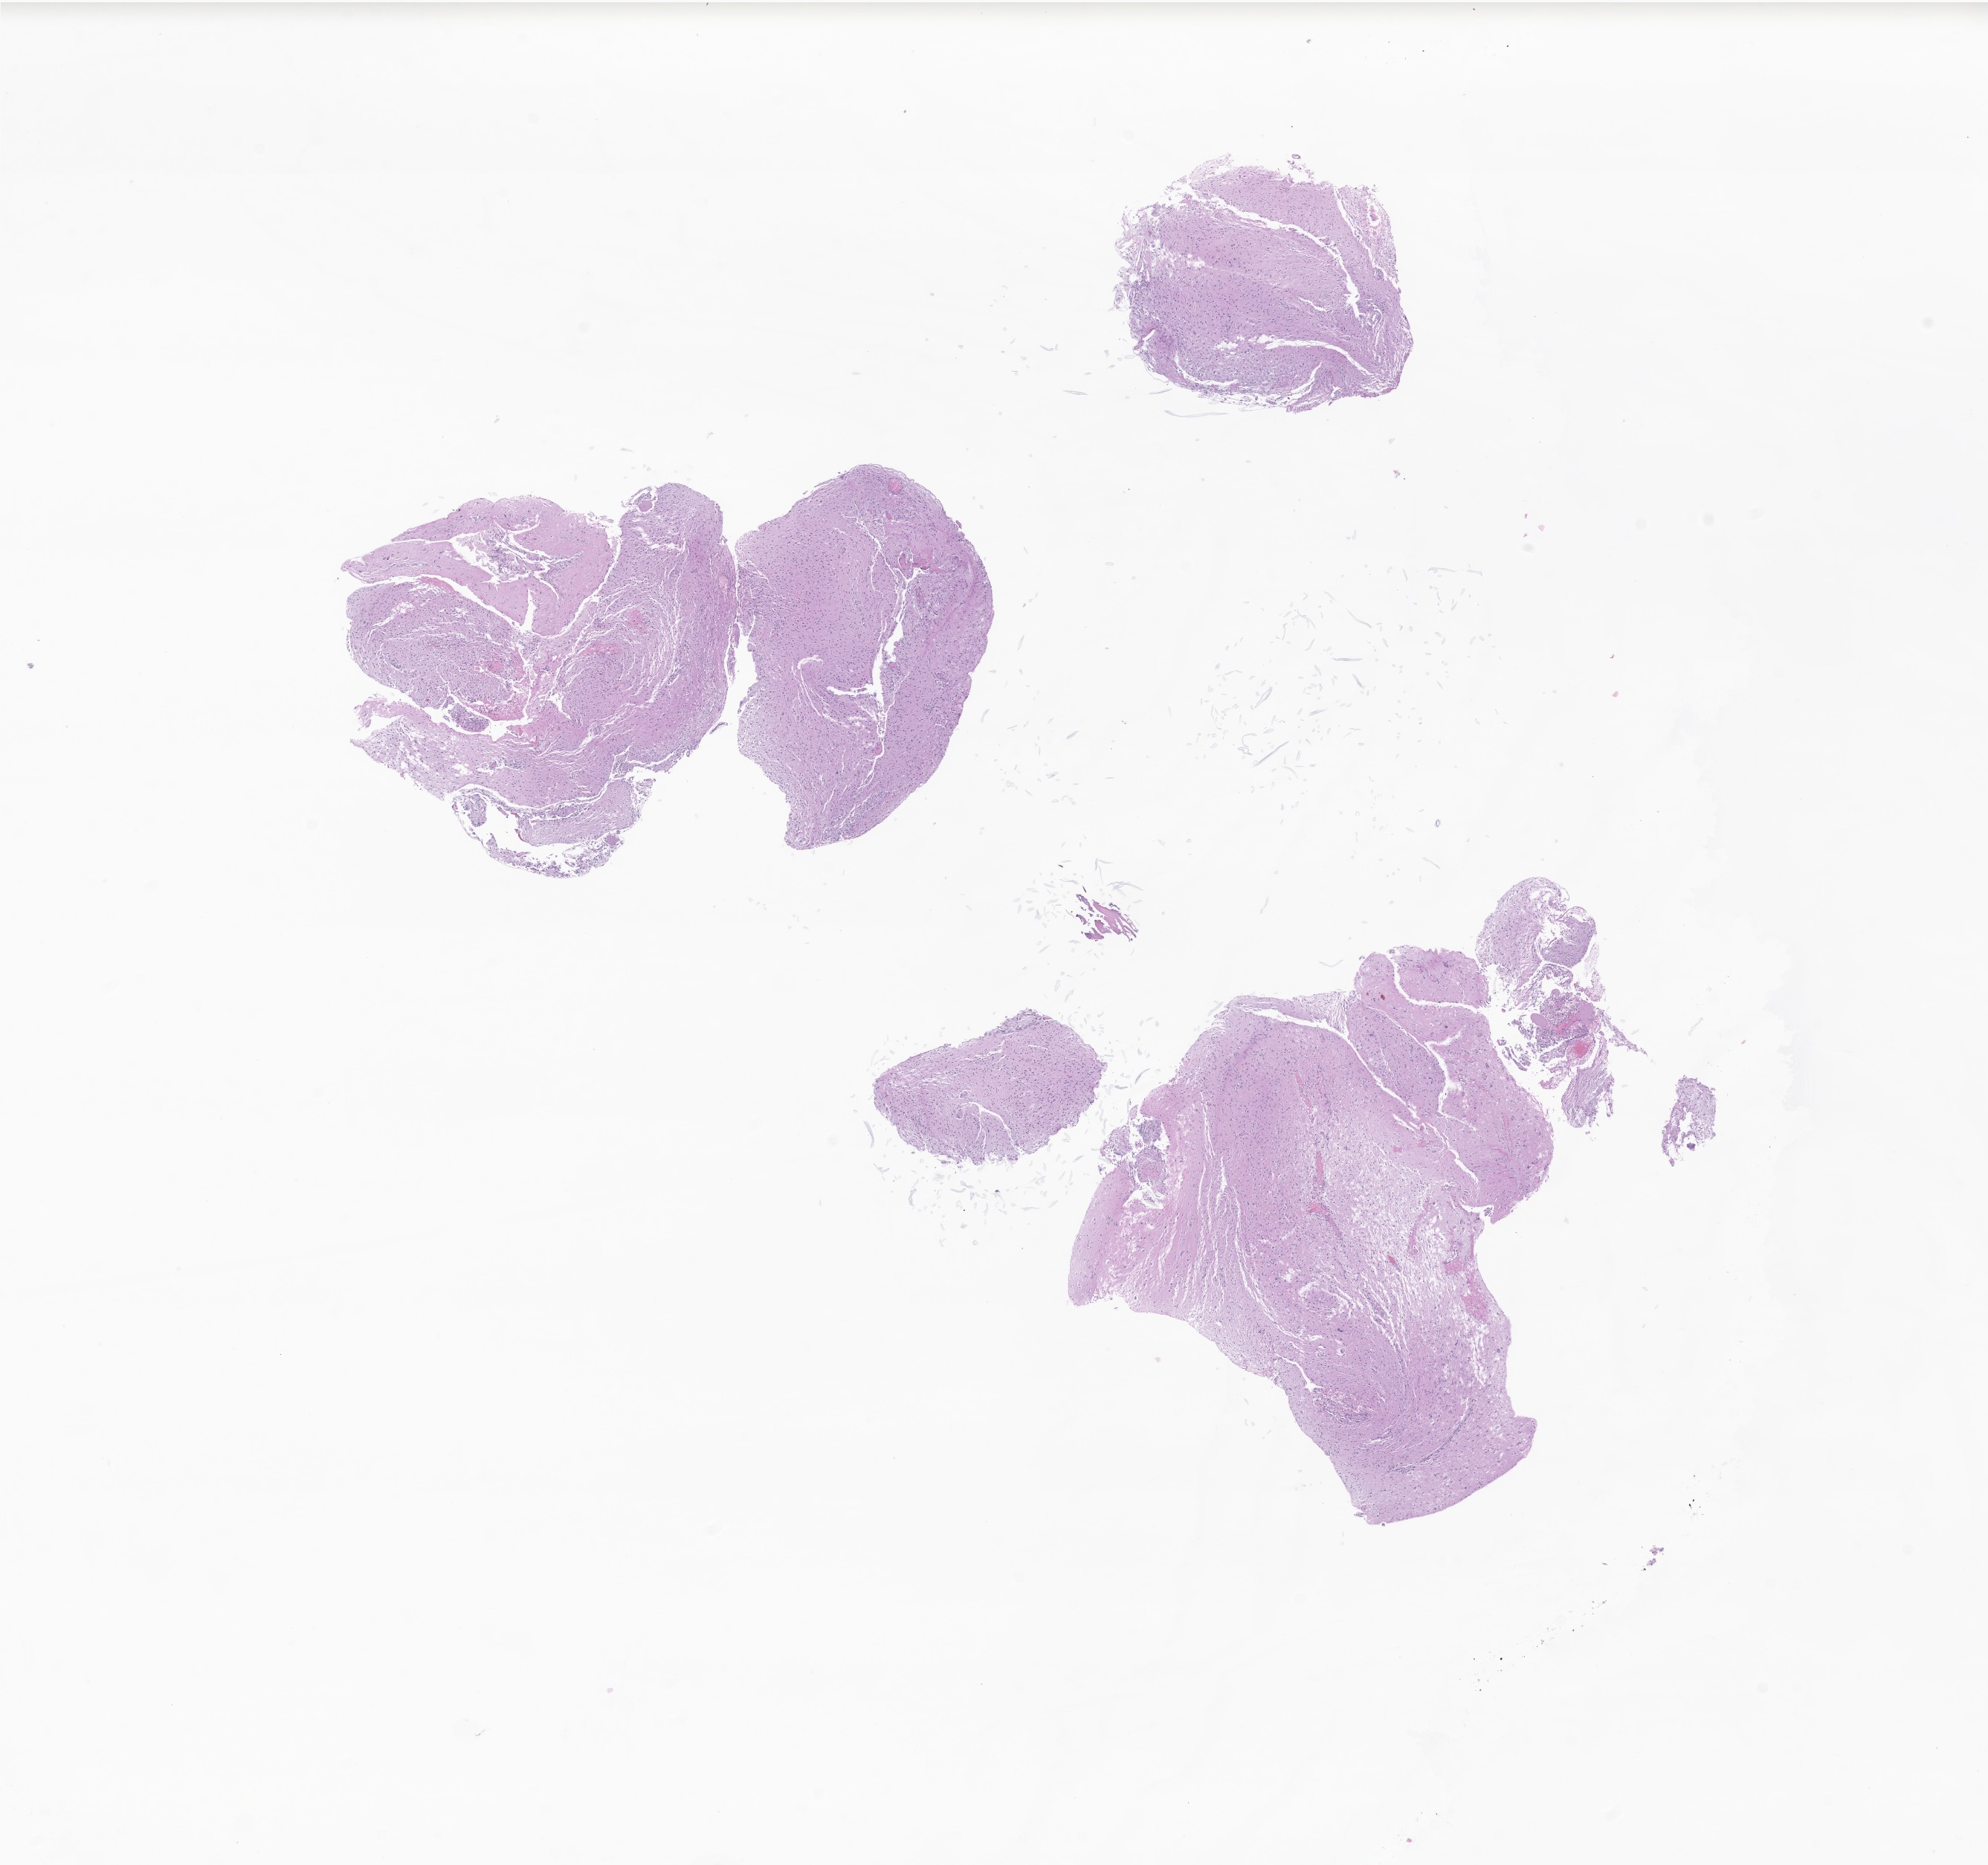
Whole-slide image, H&E stain of tumor tissue from the brain, a low-resolution overview of the entire scanned area, about 11.3 x 10.6 mm. Formalin-fixed, paraffin-embedded (FFPE) tissue. Patient male; age 62 months (5 years 2 months).
• diagnosis (ICD-O-3 morphology term): Pilocytic astrocytoma